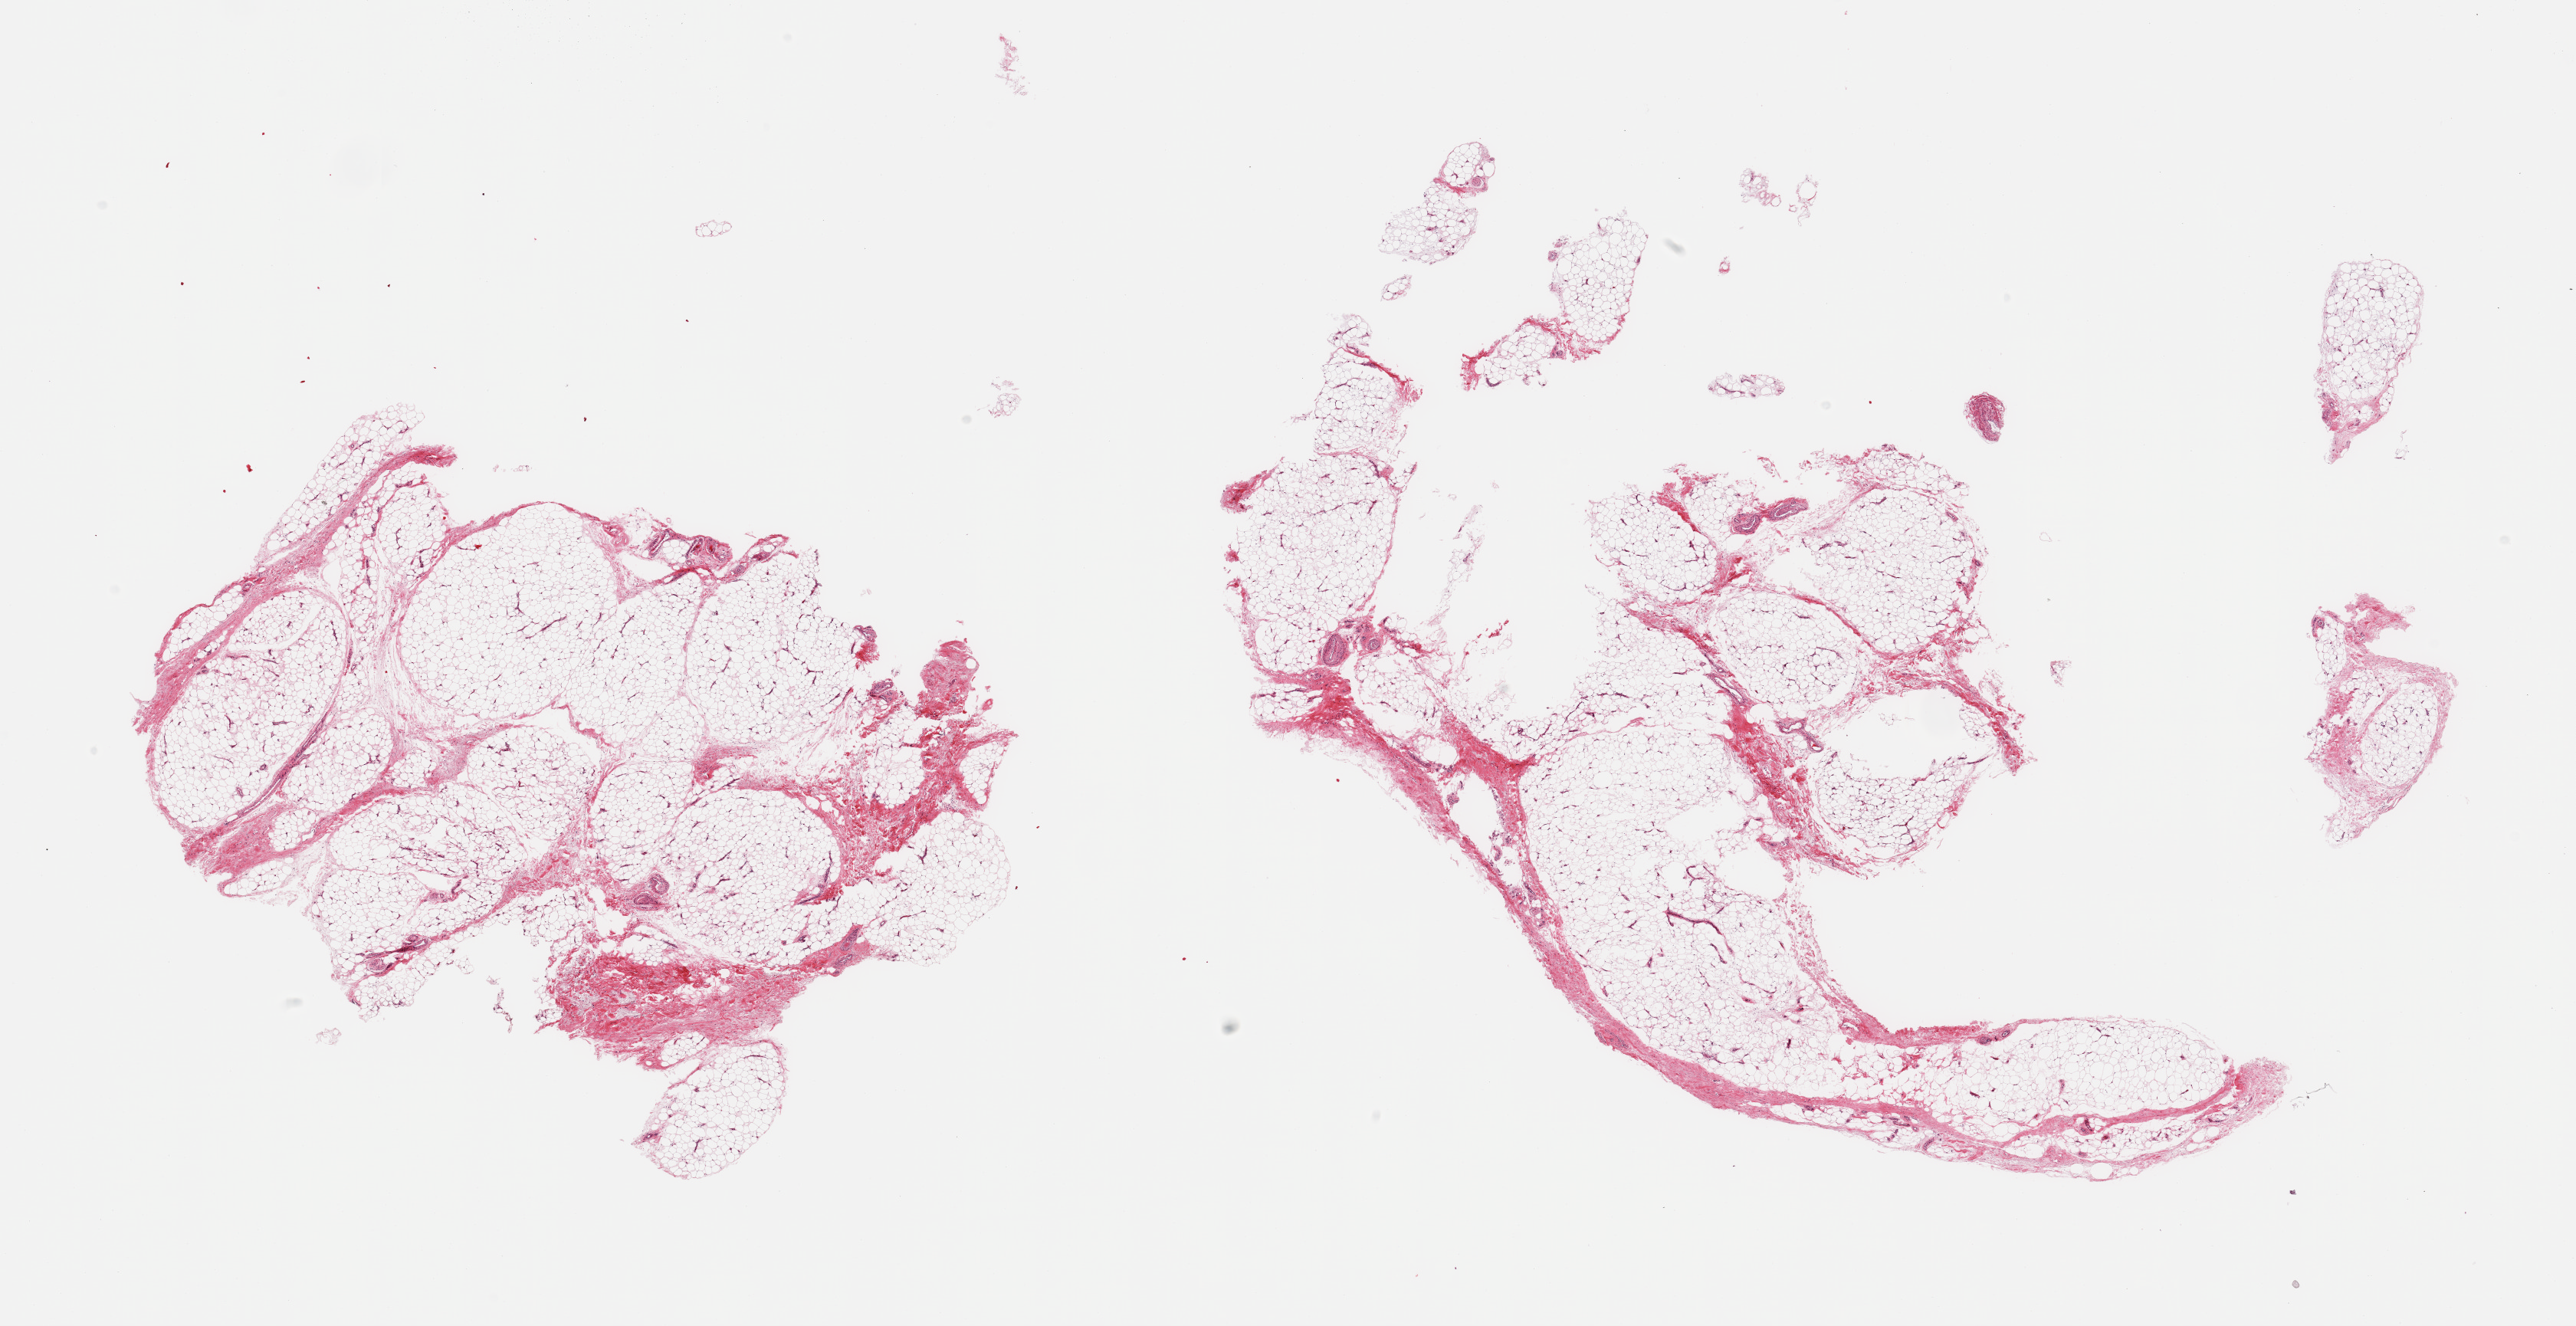
Digitized hematoxylin and eosin (H&E)-stained section, shown as a low-resolution overview of the whole scanned area (about 26.6 x 13.7 mm, acquisition: 20x scan); PAXgene-fixed, paraffin-embedded tissue; target tissue: adipose tissue; tissue donor sample. Male donor.
• pathologist's review note for this sample: 2 pieces; ~10% fibrovascular component